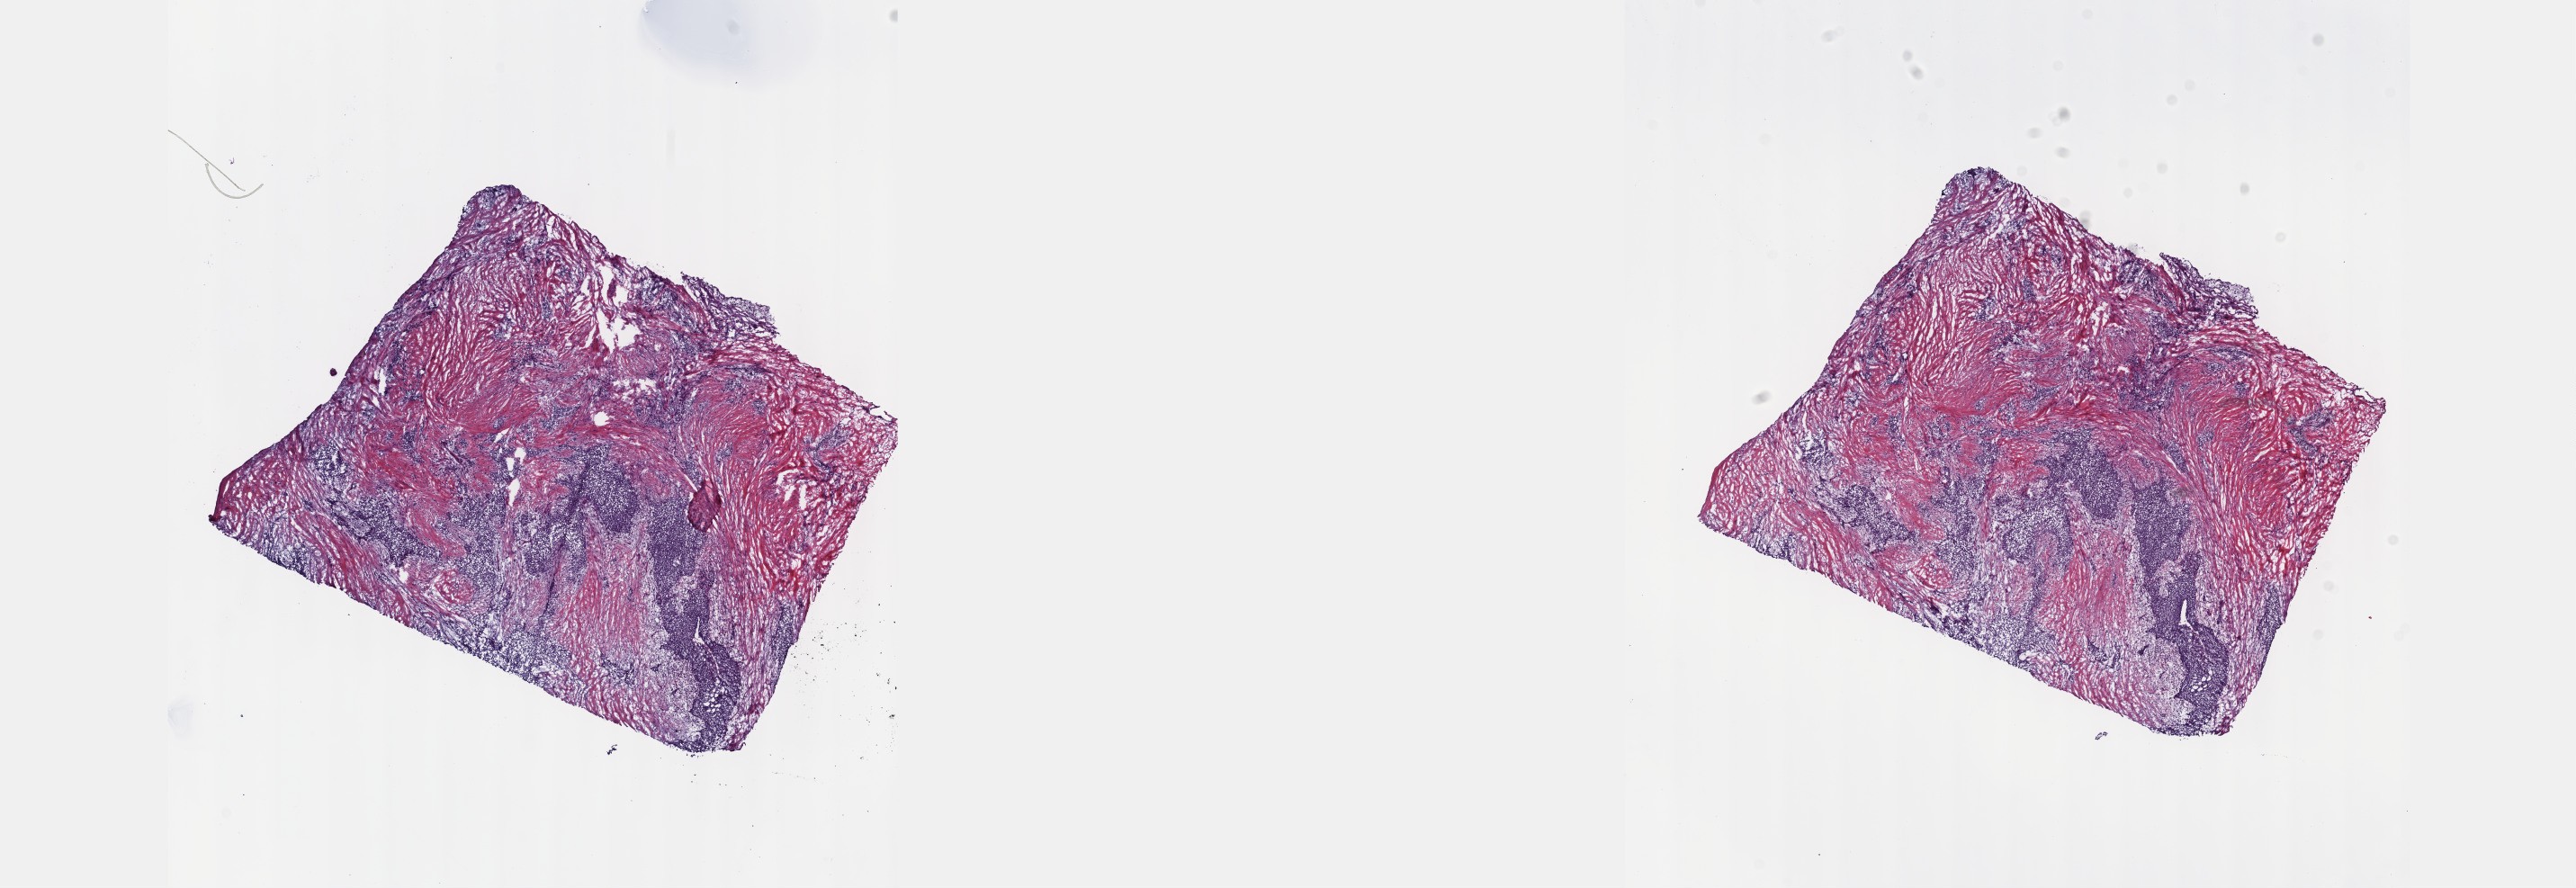
H&E whole-slide image — whole scanned area (about 23.1 x 8.0 mm, from a 40x scan) shown as a low-resolution overview, frozen section, sample: primary tumour, thymus. Male, age 76 years at initial diagnosis. Slide review estimates, as recorded: tumour cells 100%, tumour nuclei 60%, normal cells 0%, stromal cells 0%, necrosis 0%. Infiltration values recorded for this section: lymphocyte infiltration 2%, monocyte infiltration 0%, neutrophil infiltration 0%.
Diagnosis: Thymic carcinoma, NOS.